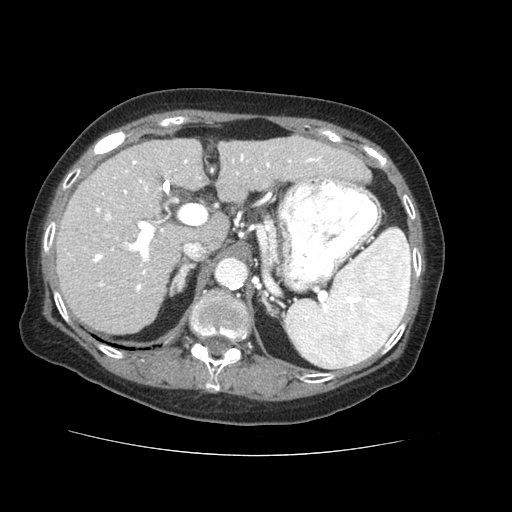
Contrast-enhanced abdominal CT (liver protocol), one axial slice; slice 38 of 73 in the series (ordered by position); reconstruction kernel STANDARD; 120 kVp; soft-tissue window (W 400 / L 40 HU); 2.5 mm slice thickness; 512 × 512 image matrix, field of view 360 × 360 mm. Case-level facts recorded for this patient, not image findings: diagnosis: hepatocellular carcinoma (patient treated with transarterial chemoembolisation; whether this scan precedes or follows treatment is not stated here); TNM stage (as recorded): Stage-IVB; Child-Pugh class: A; tumour differentiation: well differentiated.
Annotated regions visible in this slice (semi-automatic segmentation, software-assisted and operator-edited):
- liver parenchyma outside the tumour (the mass and vessels are separate outlines, so this box may not span the whole liver): bounding box (x1, y1, x2, y2) in pixels: (56, 136, 370, 334)
- liver vessels: (68, 153, 322, 292)